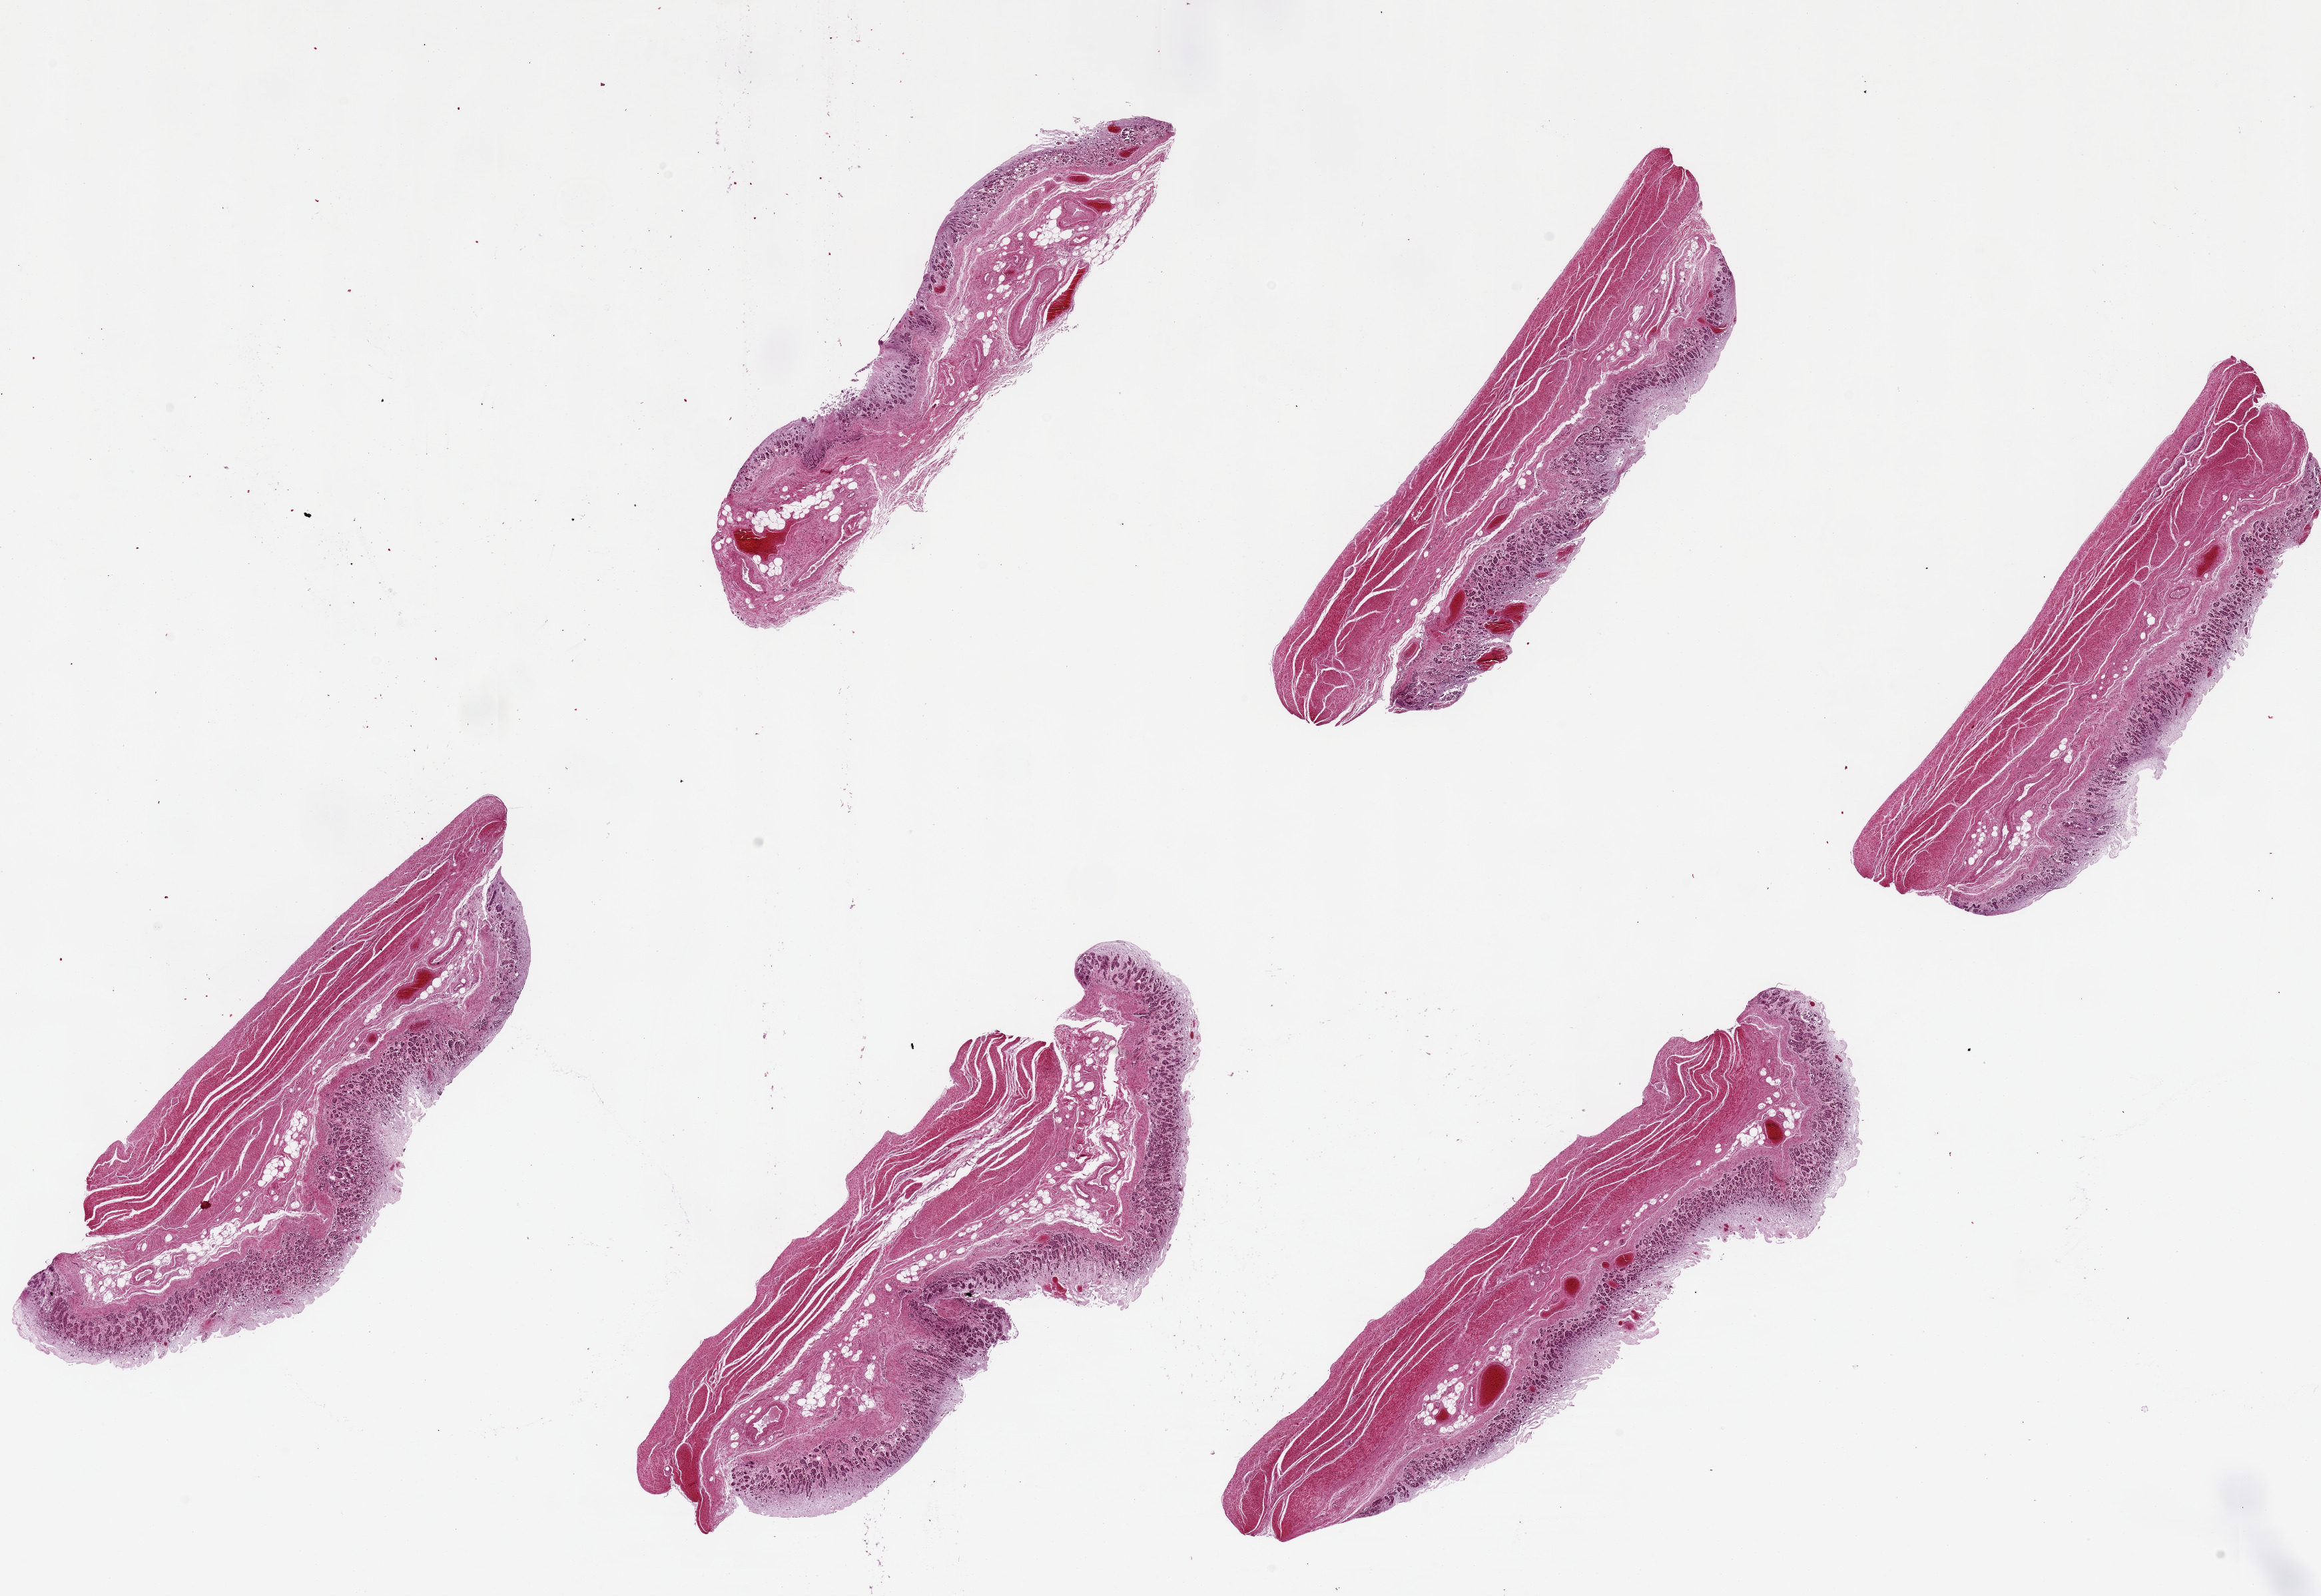
Digitized haematoxylin and eosin-stained section, brightfield, low-resolution overview of the scanned area, about 27.6 x 19.0 mm. PAXgene-fixed paraffin-embedded (PFPE) section. Target tissue: stomach. Donor tissue sample. Donor sex: female.
Review note (as recorded): 6 pieces, up to 9x3mm; mucosa is ~30% oof thickness, badly autolyzed.